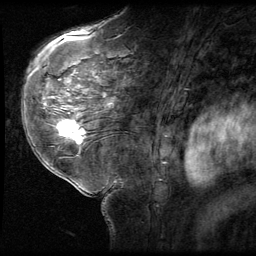
Breast MRI (dynamic contrast-enhanced), one sagittal slice. Position 39 of 58 along the scan axis. 3 images stored at this slice position (order not interpretable as contrast timing). 1.5 T. TE 4.2 ms, TR 9 ms. 256 × 256 image matrix. Female patient, age 58 years. Case-level facts recorded for this patient, not image findings: setting: breast cancer imaged before/during neoadjuvant chemotherapy; receptor status: HR-positive, HER2-negative.
Structures marked on this image (semi-automatic segmentation, software-assisted and operator-edited):
- analysis volume of interest (the breast-tissue region the enhancement analysis was run in; not a lesion): bounding box [x1, y1, x2, y2] px = [51, 116, 93, 151]
- tumour enhancement mask (voxels above the 140 % enhancement threshold inside the analysis volume of interest): [58, 120, 85, 143]